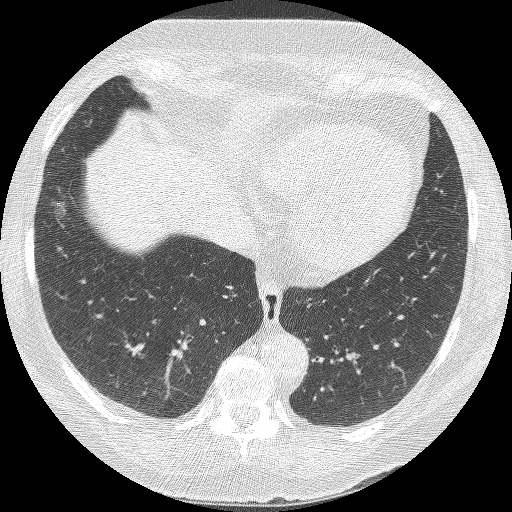
Axial slice from a low-dose chest CT screening exam, second screening round (one year after baseline), lung window (W 1500 / L -600 HU), 1.25 mm slice thickness, slice 86 of 245 in the series. Female participant, aged 68 years at enrolment. Current smoker at enrolment.
Expert-annotated lung lesion, box from (x=35, y=189) to (x=75, y=239) px. The exam's reader record, not a measurement of the box and not confirmed to be the same lesion: non-calcified nodule or mass ≥4 mm, right lower lobe, 18 × 15 mm, poorly defined margins, ground glass attenuation, pre-existing on the prior screen: yes; interval growth: yes. Lung cancer was diagnosed 42 days after this screen: bronchiolo-alveolar adenocarcinoma, NOS, right lower lobe, well differentiated (G1), stage IA (AJCC 6th edition), 13 mm at pathology.